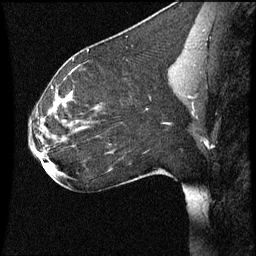
Breast MRI (dynamic contrast-enhanced), one sagittal slice. Position 32 of 60 along the scan axis. Dynamic contrast-enhanced series, image 2 of 3 at this slice position (ordered by acquisition). 1.5 T. TE 4.2 ms, TR 8.9 ms. 2 mm slice thickness. 256 × 256 image matrix, field of view 200 × 200 mm. Female patient, age 35 years. From the clinical record (not read from this slice): setting: breast cancer imaged before/during neoadjuvant chemotherapy; receptor status: HER2-positive.
Annotated regions visible in this slice (semi-automatic segmentation, software-assisted and operator-edited):
- analysis volume of interest (the breast-tissue region the enhancement analysis was run in; not a lesion): bounding box <27,66,177,177> (left, top, right, bottom; pixels)
- tumour enhancement mask (voxels above the 70 % enhancement threshold inside the analysis volume of interest): <42,92,79,159>